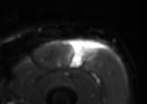
MRI of an extremity soft-tissue mass, one axial slice. Position 36 of 85 along the scan axis. T2-weighted fat-saturated. MR volume resampled by the dataset authors to the PET/CT grid (not the native acquisition matrix). 147 × 104 image matrix, field of view 144 × 102 mm. Male patient. From the clinical record (not read from this slice): histological type: extraskeletal osteosarcoma; grade: high; site of the primary tumour: thigh.
Outlined on this slice (expert contour drawn on MRI and transferred to this co-registered scan by the dataset authors):
- gross tumour volume (mass): box from (x=71, y=42) to (x=86, y=68) px